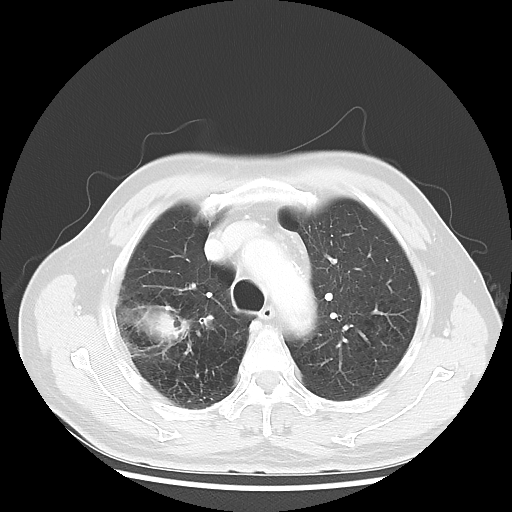
Chest CT, one axial slice; slice 38 of 50 in the series (ordered by position); reconstruction kernel LUNG; 120 kVp; lung window (W 1500 / L -600 HU); 5 mm slice thickness; 512 × 512 image matrix, field of view 360 × 360 mm. Male patient, age 69 years. Case-level facts recorded for this patient, not image findings: clinical TNM (as recorded): T3 N0 M0; histopathological grade: G3.
Annotated regions visible in this slice (bounding box drawn by a radiologist):
- lung tumour (recorded histology: adenocarcinoma): box from (x=111, y=289) to (x=197, y=360) px